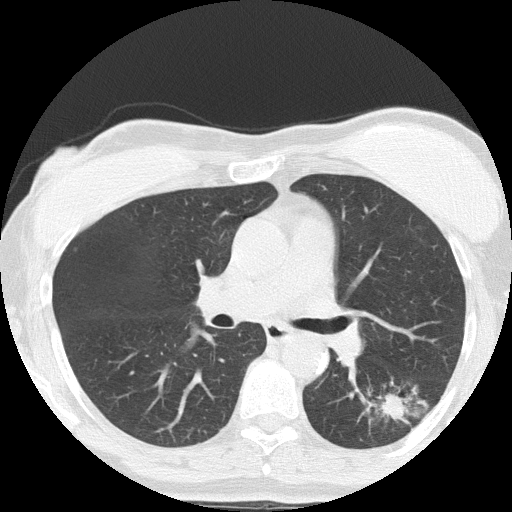
Low-dose screening chest CT, one axial slice; slice 88 of 152 in the series (ordered by position); reconstruction kernel FC51; lung window (W 1500 / L -600 HU); 2 mm slice thickness; 512 × 512 image matrix, field of view 308 × 308 mm.
Structures marked on this image (manually delineated by an expert):
- lesion 1 (tumor, lower lobe of left lung): bounding box [x1, y1, x2, y2] px = [383, 396, 405, 418]